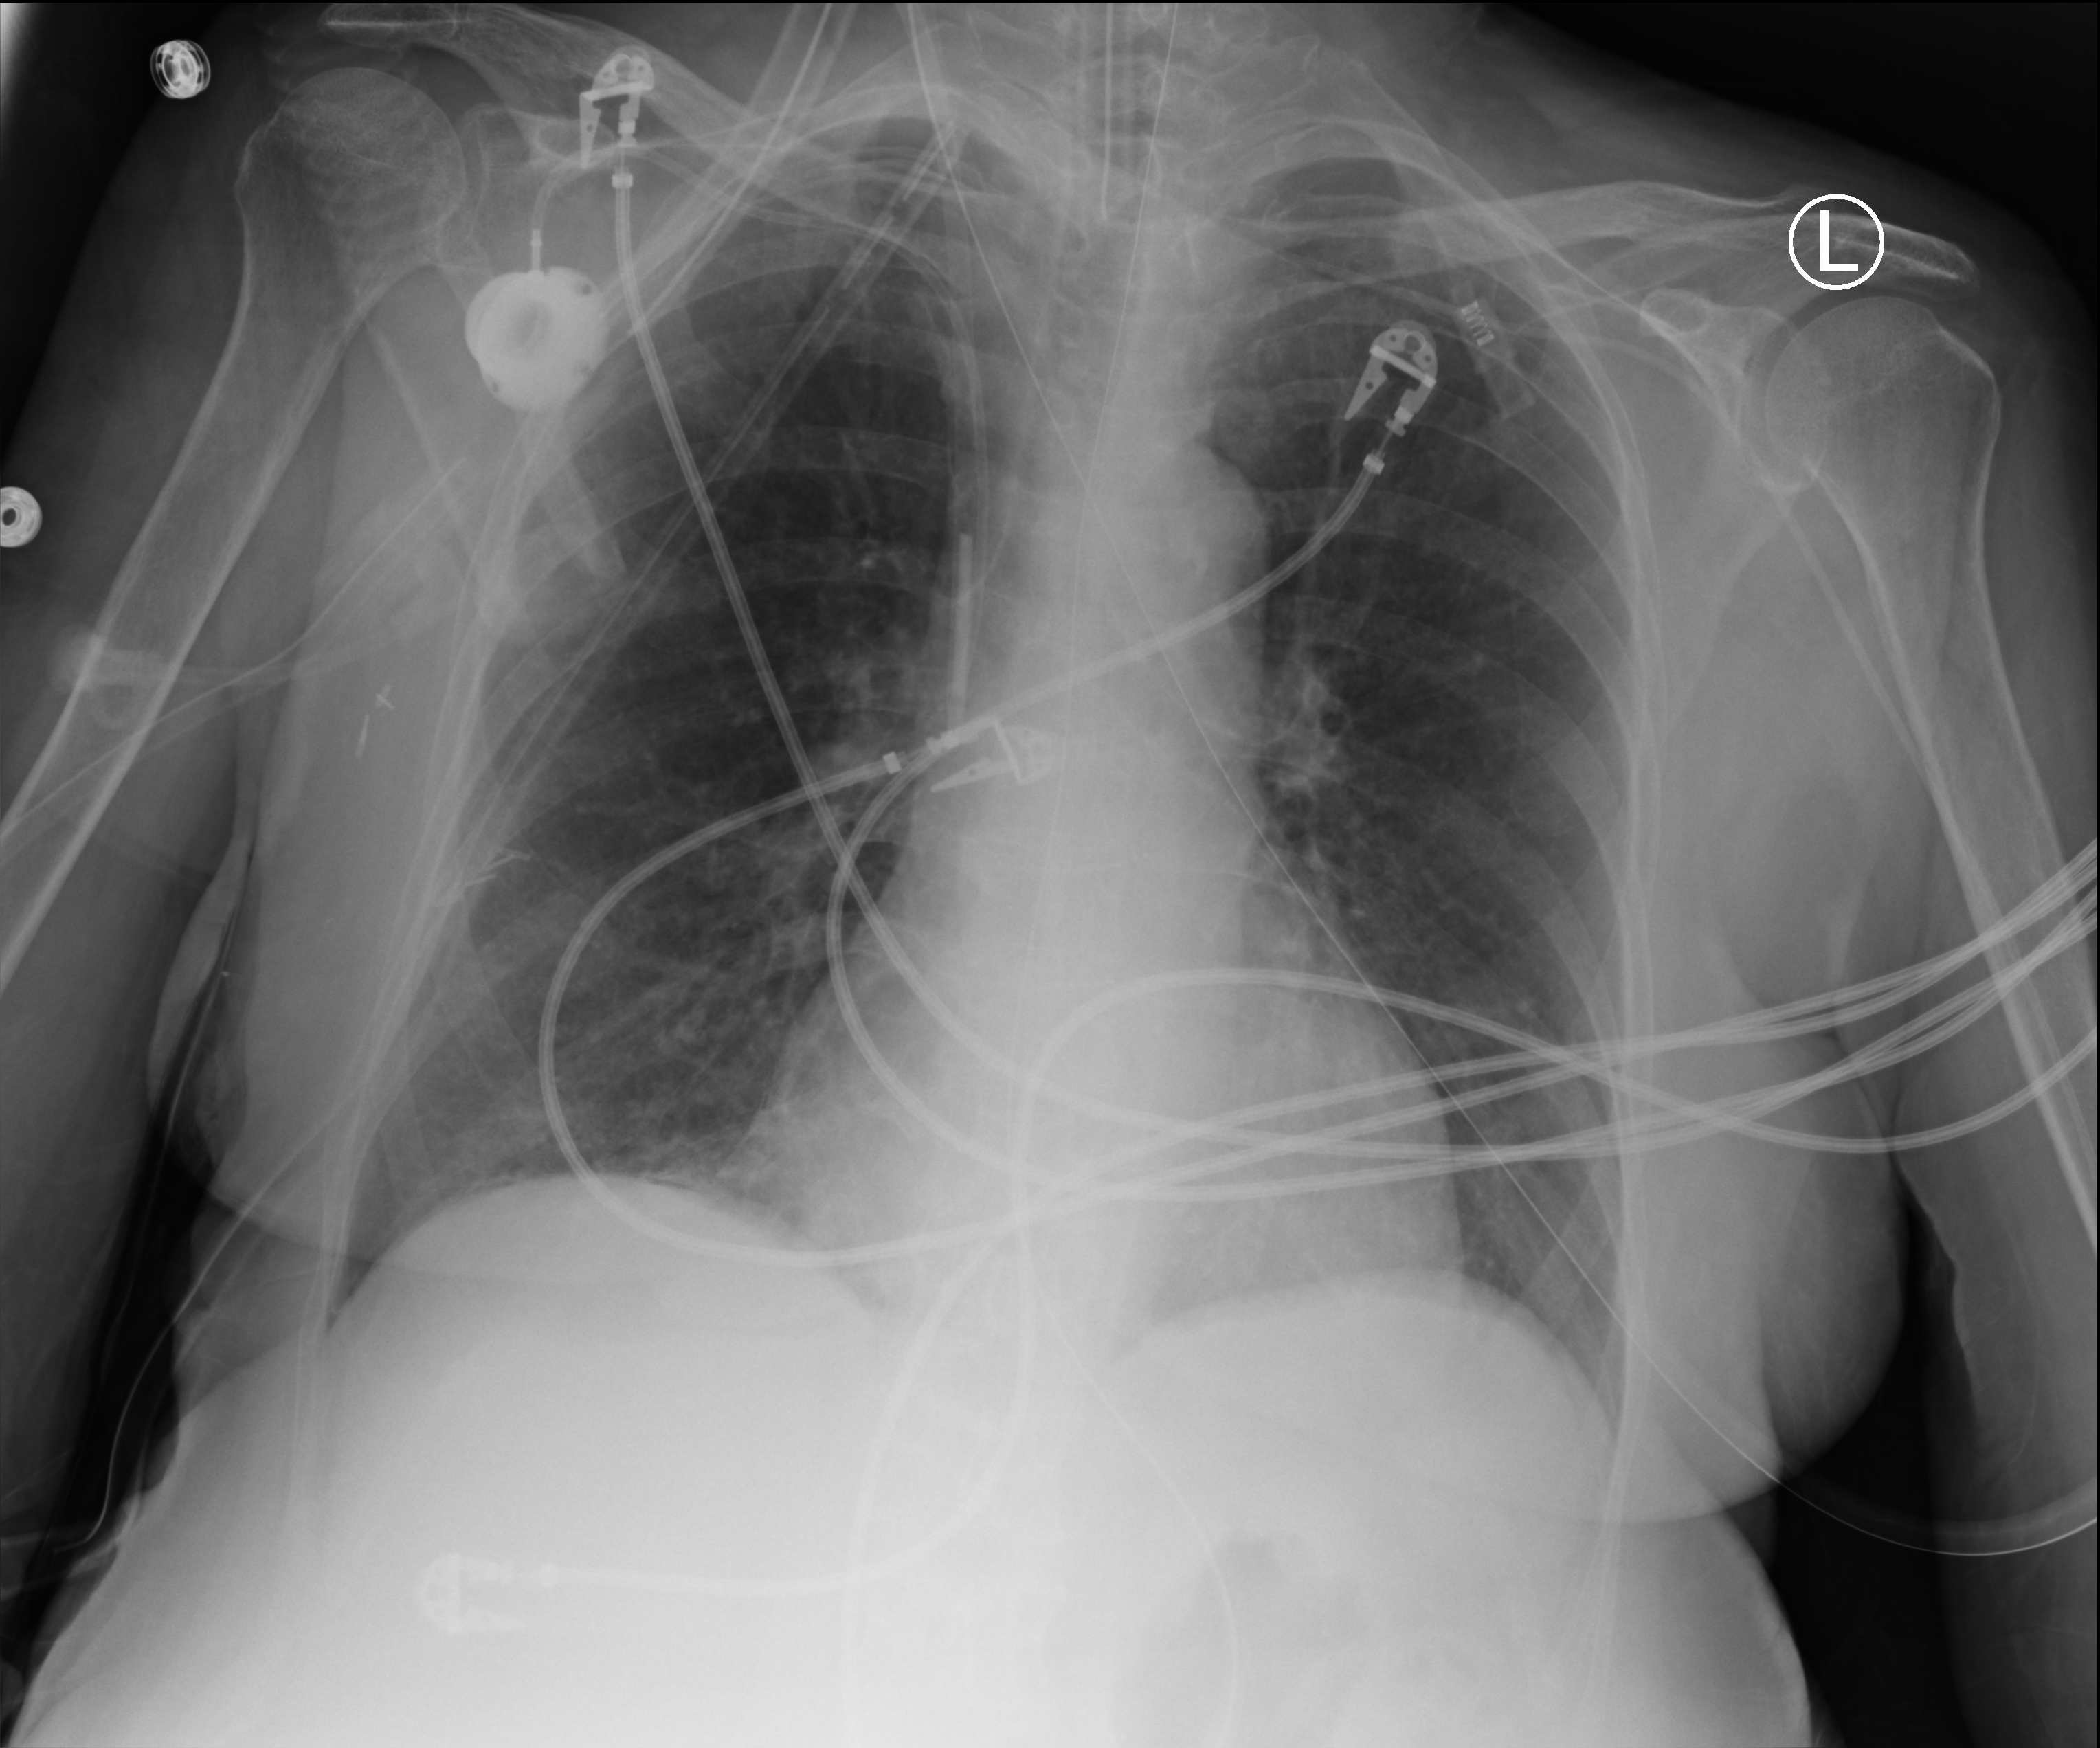
Portable chest radiograph; anteroposterior (AP) projection. Female patient hospitalised with COVID-19, age 60–74 years.
From the hospital-stay record, not from the radiograph (when in the stay this image was taken is not recorded):
- admitted to intensive care during this hospital stay: yes
- mechanically ventilated during this hospital stay: yes
- other chronic lung disease (admission record): no